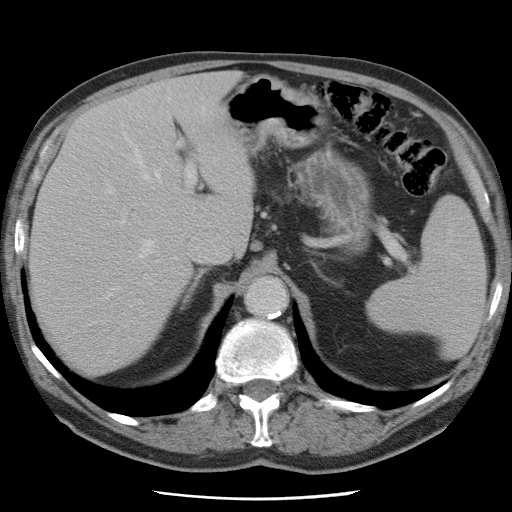
Contrast-enhanced abdominal CT, one axial slice; position 52 of 78 along the scan axis; 120 kVp; intravenous contrast given; soft-tissue window (W 400 / L 40 HU); 512 × 512 image matrix, field of view 337 × 337 mm. Male patient, age 75 years. Case-level facts recorded for this patient, not image findings: diagnosis: colorectal cancer liver metastases, imaged before liver resection; multiple liver metastases: yes; largest metastasis: 2.4 cm; disease in both lobes: yes.
Annotated regions visible in this slice (manually delineated by an expert):
- hepatic veins: bounding box [x1, y1, x2, y2] px = [58, 107, 205, 298]
- liver: [30, 74, 251, 372]
- planned liver remnant (the part of the liver to remain after resection): [30, 125, 192, 372]
- portal vein (with intrahepatic branches): [107, 141, 196, 225]